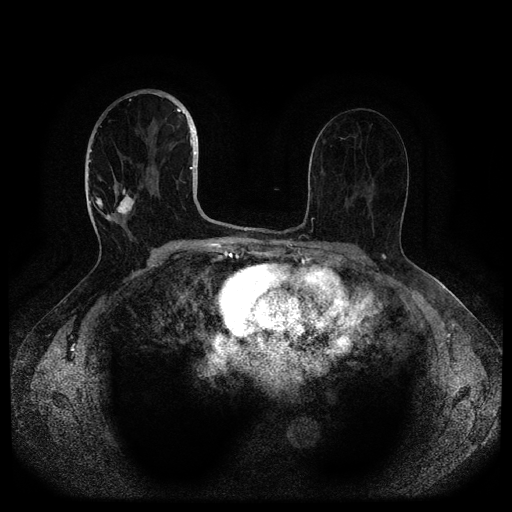
Breast MRI (dynamic contrast-enhanced, multi-phase), one axial slice; position 54 of 116 along the scan axis; dynamic contrast-enhanced series, time point 2 of 5 at this slice position (early post-contrast); 1.5 T; TE 2.6 ms, TR 5.3 ms; 2 mm slice thickness; 512 × 512 image matrix, field of view 350 × 350 mm. Patient: female, 82 years.
Structures marked on this image (semi-automatic segmentation, software-assisted and operator-edited):
- breast lesion (labelled 'tumour' in the annotation; benign lesions carry a separate 'benign' label): bounding box [x1, y1, x2, y2] px = [113, 188, 136, 217]